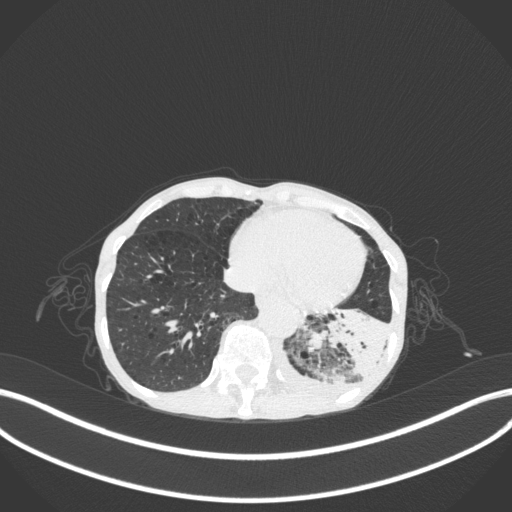
Chest CT, one axial slice; position 55 of 347 along the scan axis; 120 kVp; lung window (W 1500 / L -600 HU); 512 × 512 image matrix, field of view 400 × 400 mm. Patient: female, 70 years. Case-level facts recorded for this patient, not image findings: clinical TNM (as recorded): T3 N0 M0; histopathological grade: G3.
Outlined on this slice (rectangle marked by the reading radiologist):
- lung tumour (recorded histology: small cell carcinoma): bounding box [x1, y1, x2, y2] px = [304, 299, 390, 391]